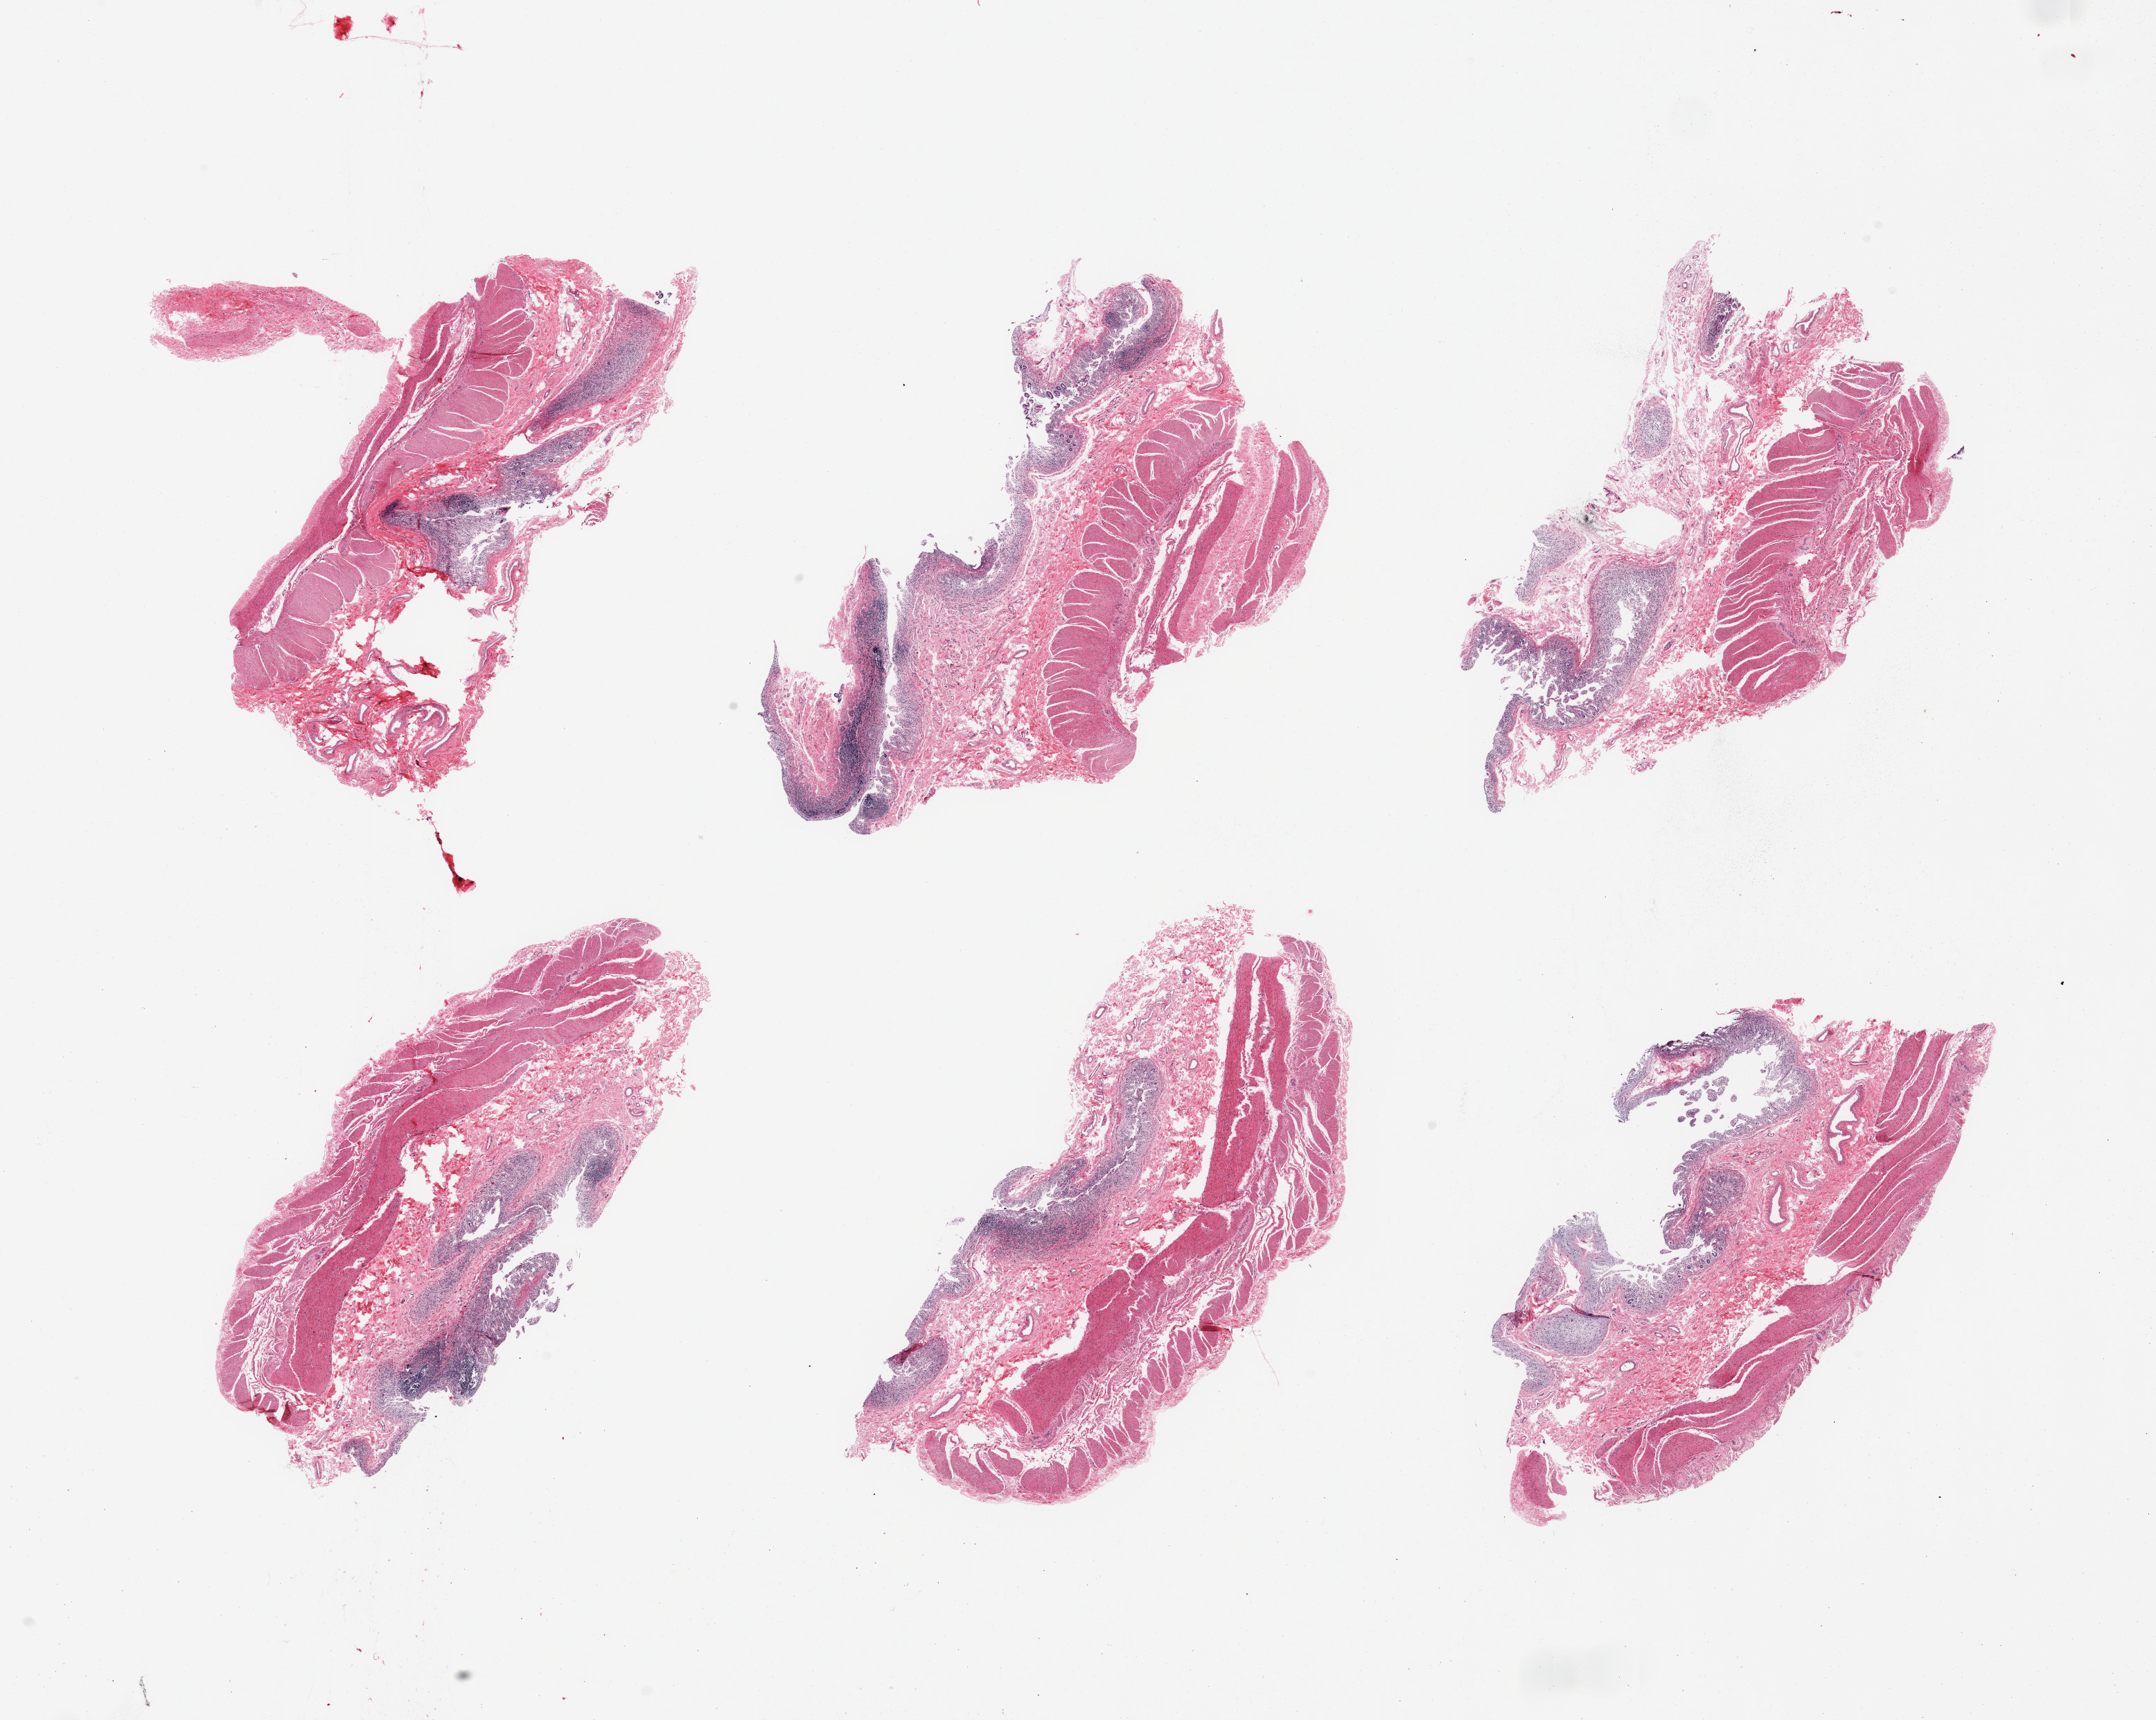
Digitized H&E-stained section — whole scanned area (about 24.6 x 19.6 mm) shown as a low-resolution overview, PAXgene-fixed, paraffin-embedded tissue, section of ileum (target tissue), donor tissue sample.
Review note (as recorded): 6 pieces; partially autolyzed mucosa, only scattered lymphoid aggregates, and muscularis (not target).